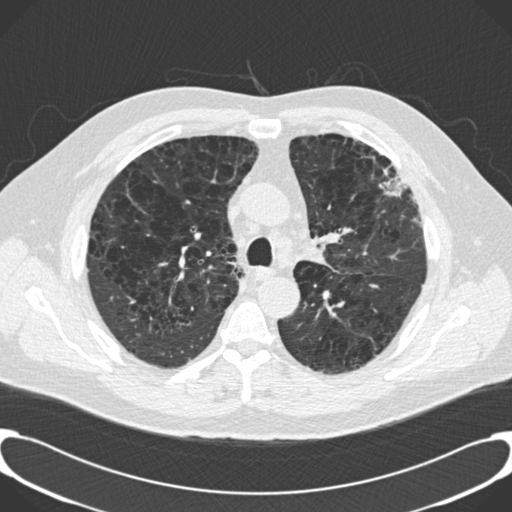
Low-dose screening chest CT, one axial slice. Reconstruction kernel B30f. Lung window (W 1500 / L -600 HU). 2 mm slice thickness. 512 × 512 image matrix, field of view 380 × 380 mm.
Annotated regions visible in this slice (manually delineated by an expert):
- lesion 1 (tumor, upper lobe of left lung): box from (x=379, y=175) to (x=406, y=196) px